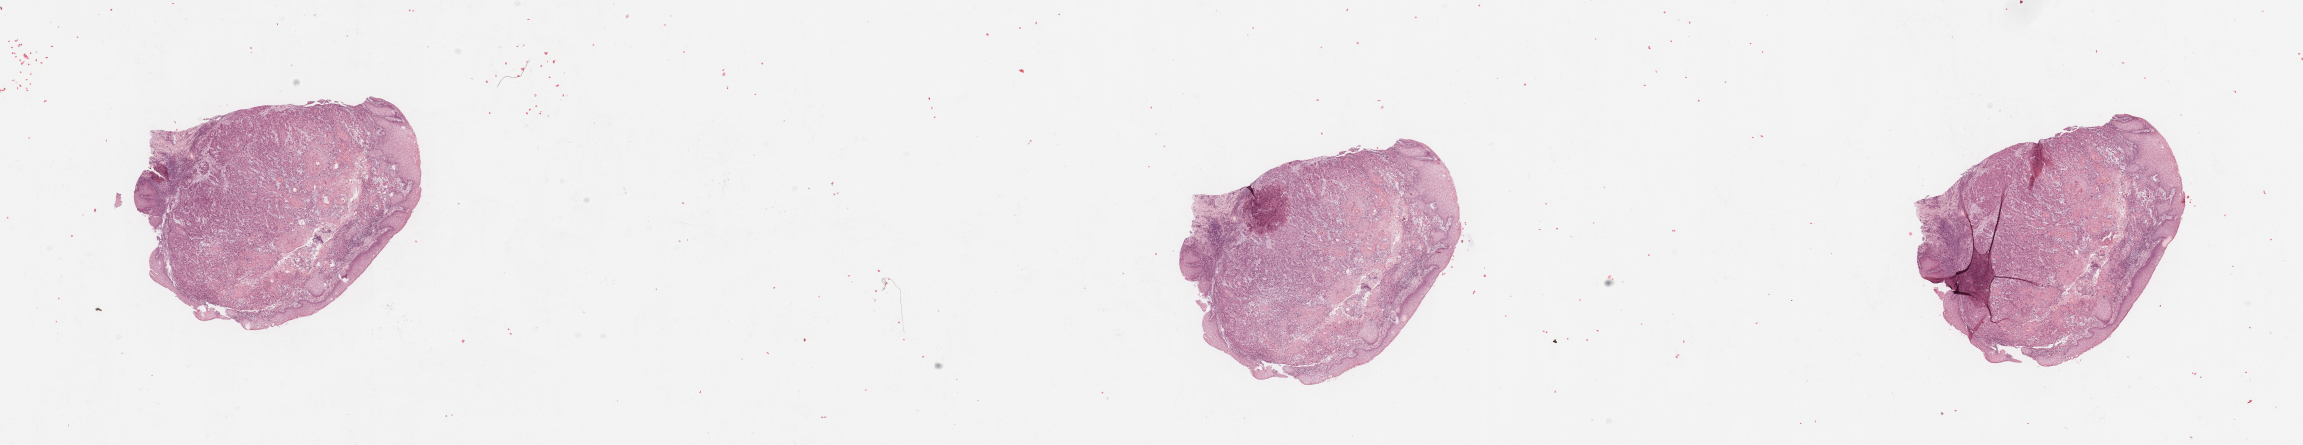
Digitized H&E-stained tissue section (whole slide) — whole scanned area (about 36.4 x 7.0 mm, from a 20x scan) shown as a low-resolution overview, tumour tissue sample, sampled site: larynx. 72-year-old male patient. Slide review estimates, as recorded: tumour nuclei 80%, necrosis 5%.
Diagnosis: Squamous cell carcinoma, NOS (larynx, NOS).